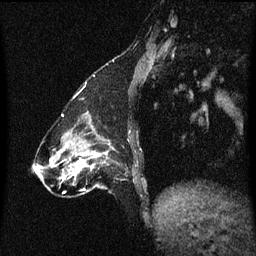
Breast MRI (dynamic contrast-enhanced), one sagittal slice; slice 15 of 60 in the series (ordered by position); dynamic contrast-enhanced series, image 2 of 3 at this slice position (ordered by acquisition); 1.5 T; TE 4.2 ms, TR 8.4 ms; 2 mm slice thickness; 256 × 256 image matrix. Female patient, age 47 years.
Structures marked on this image (semi-automatically segmented with operator editing):
- analysis volume of interest (the breast-tissue region the enhancement analysis was run in; not a lesion): box from (x=81, y=140) to (x=114, y=195) px
- tumour enhancement mask (voxels above the 70 % enhancement threshold inside the analysis volume of interest): (x=90, y=154)–(x=93, y=167)